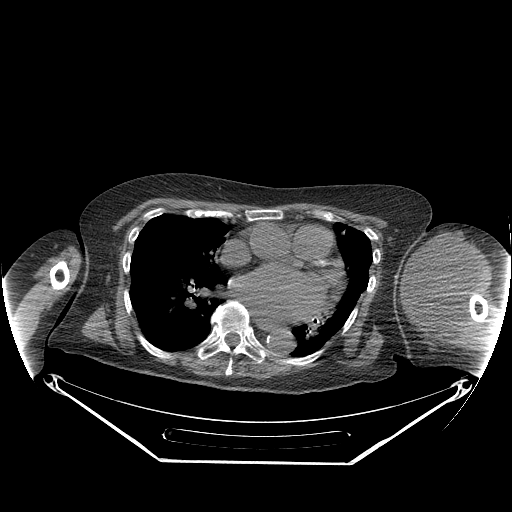
CT of an extremity soft-tissue mass (from a PET/CT study), one axial slice. Position 169 of 267 along the scan axis. 140 kVp. Soft-tissue window (W 400 / L 40 HU). 3.75 mm slice thickness. 512 × 512 image matrix, field of view 500 × 500 mm. Female patient. From the clinical record (not read from this slice): histological type: pleiomorphic leiomyosarcoma; grade: high; site of the primary tumour: left biceps.
Outlined on this slice (expert contour drawn on MRI and transferred to this co-registered scan by the dataset authors):
- gross tumour volume including surrounding oedema: bounding box <402,233,485,330> (left, top, right, bottom; pixels)
- gross tumour volume (mass): <402,233,478,325>